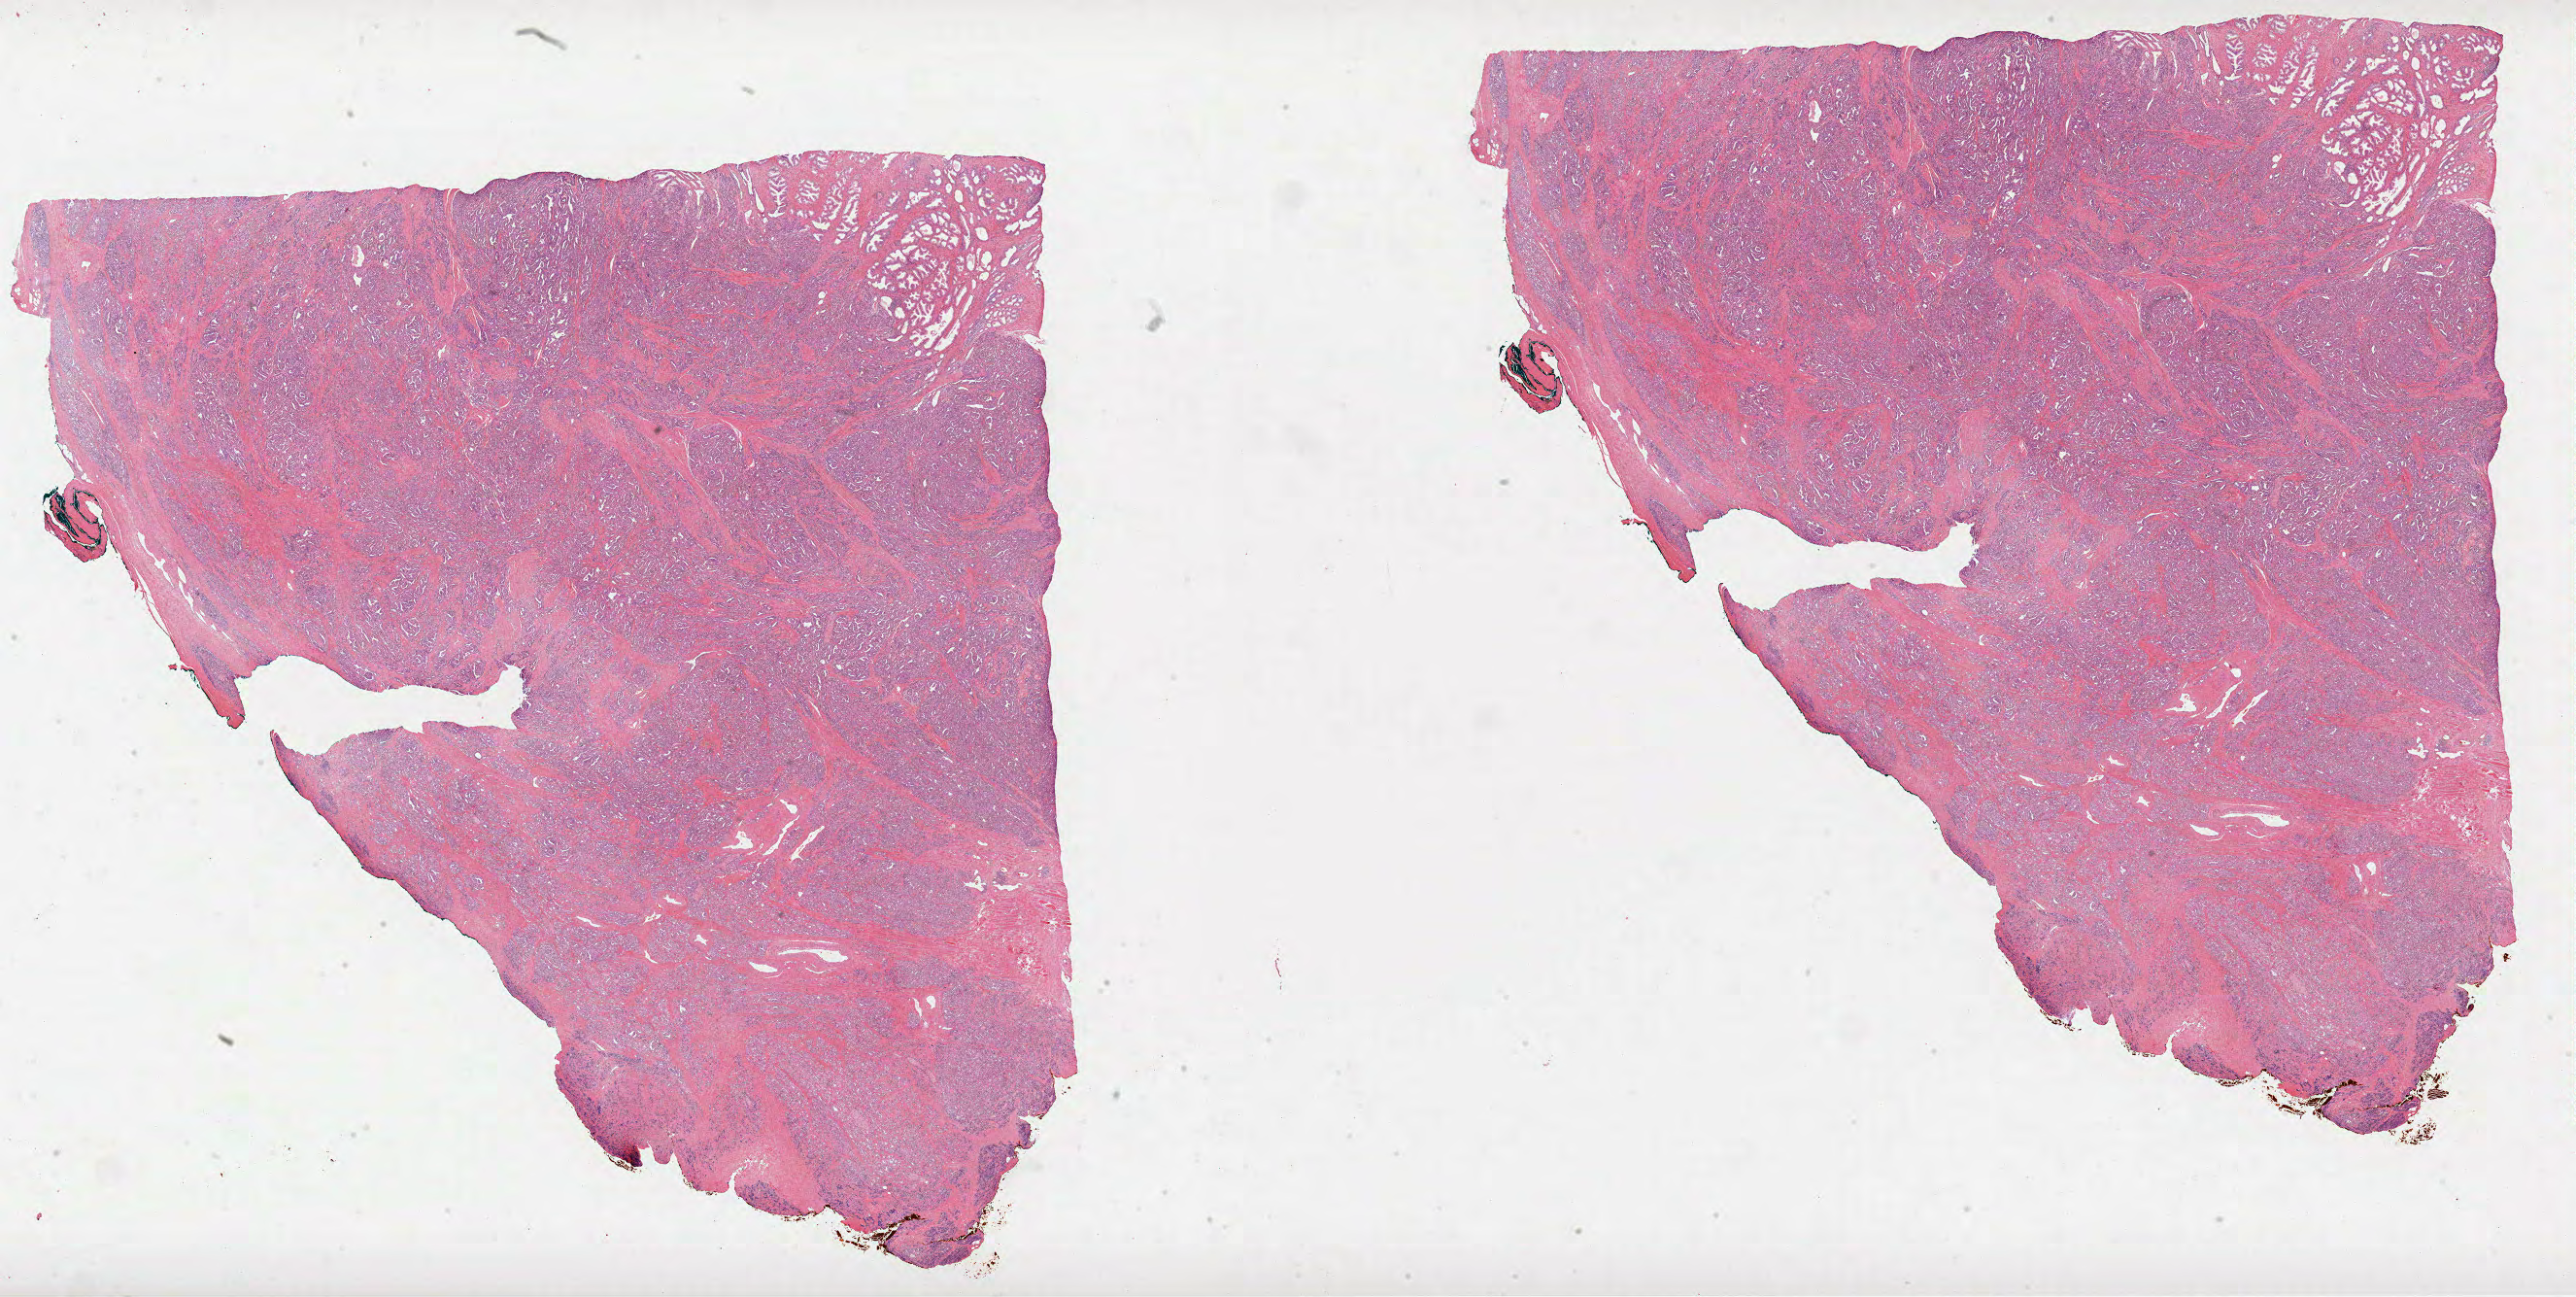
Digitized H&E tissue section (whole slide) — low-resolution overview of the scanned area, about 42.8 x 21.5 mm. Formalin-fixed paraffin-embedded (FFPE) diagnostic section. Sample: primary tumour, prostate. Male patient; age at initial diagnosis 57 years. Gleason score: 7 (4+3).
Pathologic diagnosis: Acinar cell carcinoma (prostate gland).